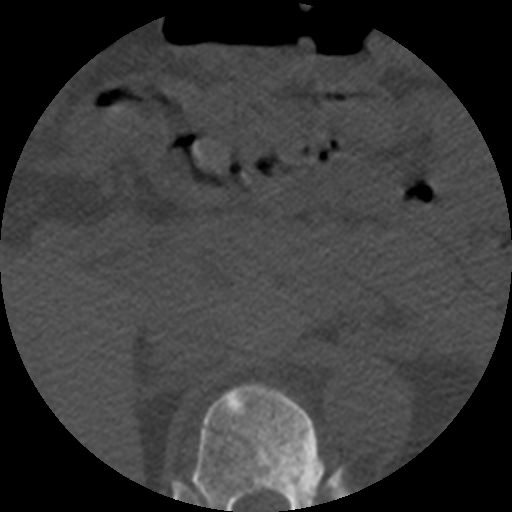
CT including the spine, one axial slice. Slice 245 of 508 in the series (ordered by position). Reconstruction kernel STANDARD. Bone window (W 1800 / L 400 HU). 1.25 mm slice thickness. 512 × 512 image matrix. Patient age 57 years. Case-level facts recorded for this patient, not image findings: primary cancer: prostate.
Outlined on this slice (semi-automatically segmented with operator editing):
- T11 vertebra: box from (x=192, y=384) to (x=324, y=512) px